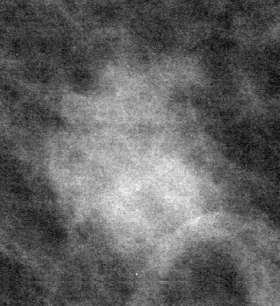
Cropped region of a digitized screen-film mammogram centred on a radiologist-marked abnormality, left breast, MLO view, BI-RADS breast density category 2 (scale 1–4).
- Marked abnormality: mass, shape irregular, margins microlobulated; BI-RADS assessment category 4; subtlety rating 5 on a 1 (subtle) to 5 (obvious) scale; pathology result (as recorded, not read from the image): malignant.